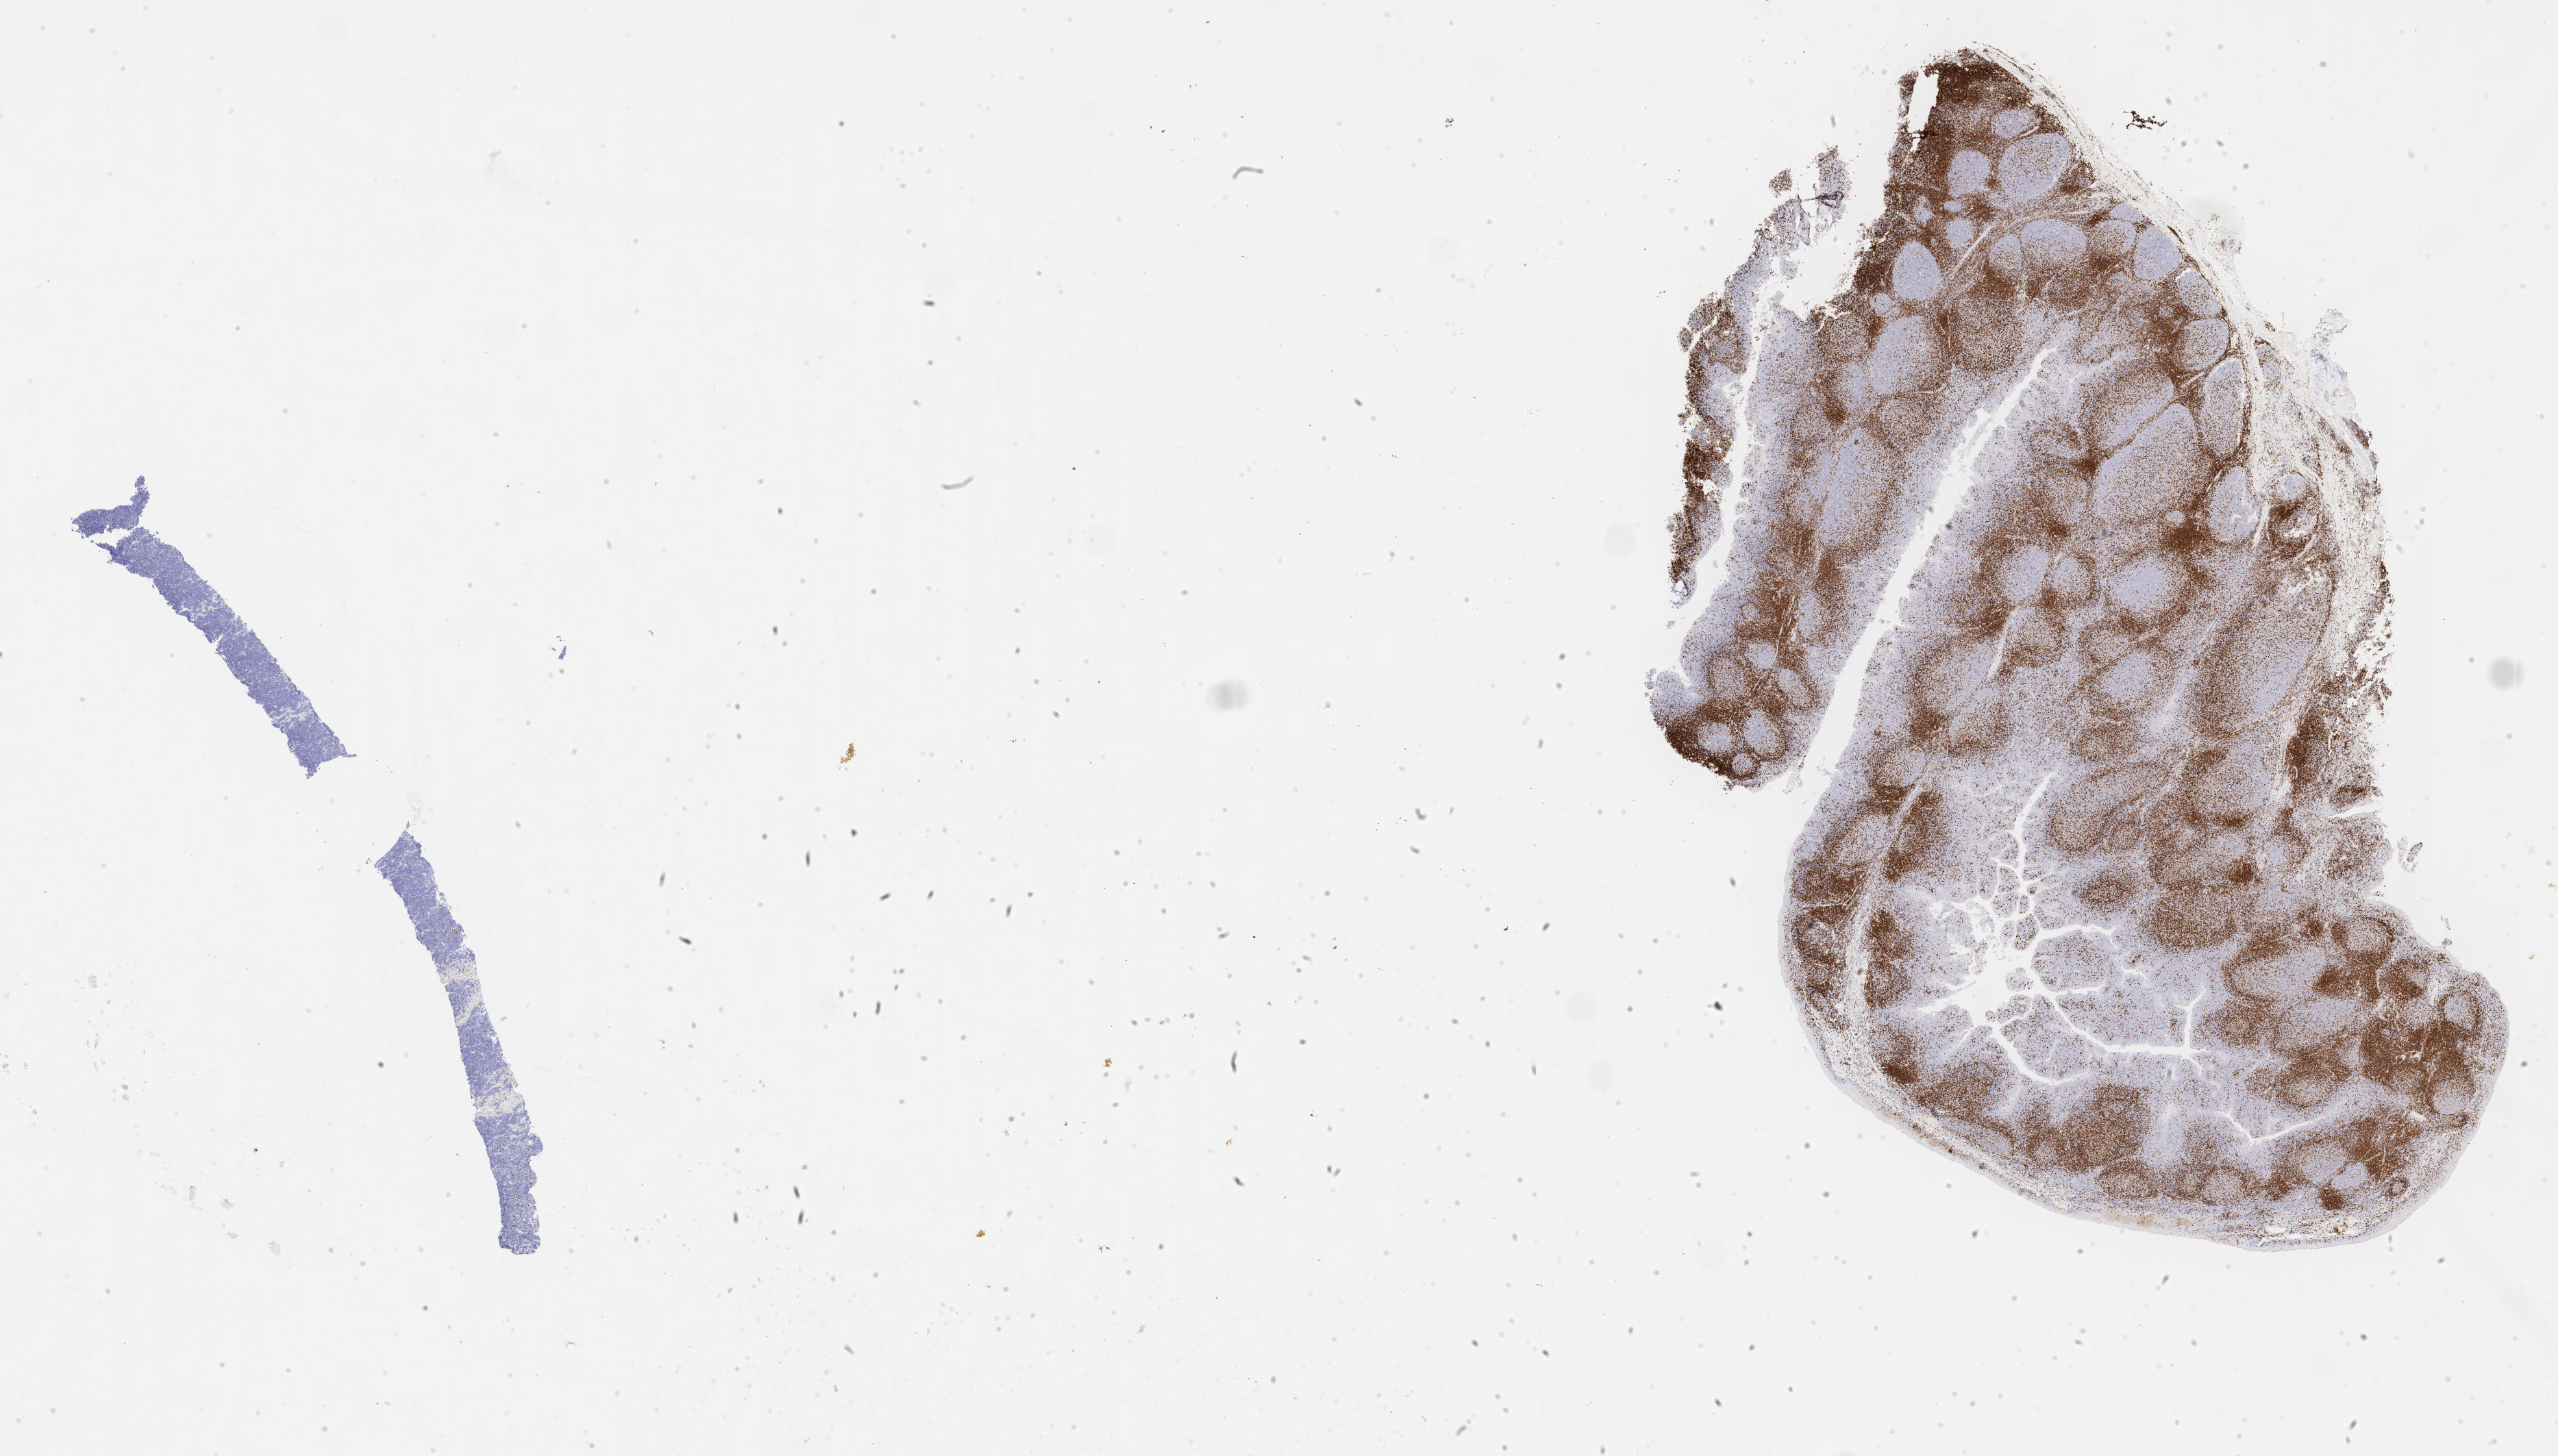
IHC for CD3, whole-slide image — whole scanned area (about 30.2 x 17.2 mm) shown as a low-resolution overview. Patient sex: female.
Specimen: tumor tissue.